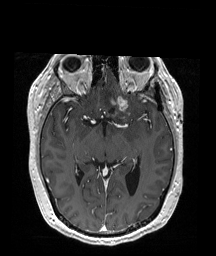
Brain MRI from a brain-tumour surgery series, one axial slice. T1-weighted post-contrast. 1 mm slice thickness. 216 × 256 image matrix, field of view 211 × 250 mm. Case-level facts recorded for this patient, not image findings: histopathology: Oligodendroglioma; WHO grade: 2.
Annotated regions visible in this slice (outlined manually by an expert reader):
- tumour: bounding box [x1, y1, x2, y2] px = [107, 95, 132, 117]